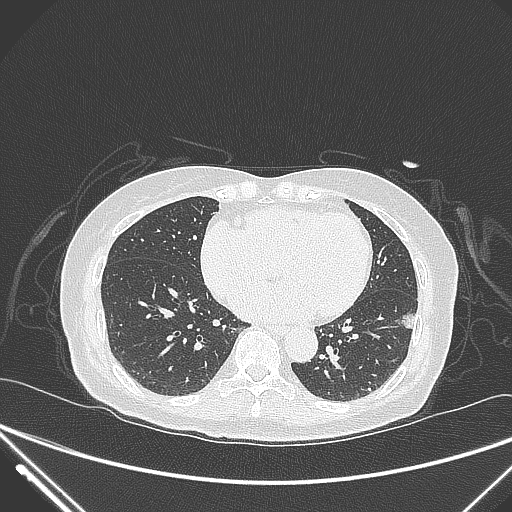
Chest CT, one axial slice; slice 116 of 310 in the series (ordered by position); lung window (W 1500 / L -600 HU); 1 mm slice thickness; 512 × 512 image matrix. Female patient, age 82 years. Case-level facts recorded for this patient, not image findings: clinical TNM (as recorded): T1c N0 M0; histopathological grade: G2.
Annotated regions visible in this slice (rectangle marked by the reading radiologist):
- lung tumour (recorded histology: adenocarcinoma): bounding box [x1, y1, x2, y2] px = [393, 304, 424, 350]